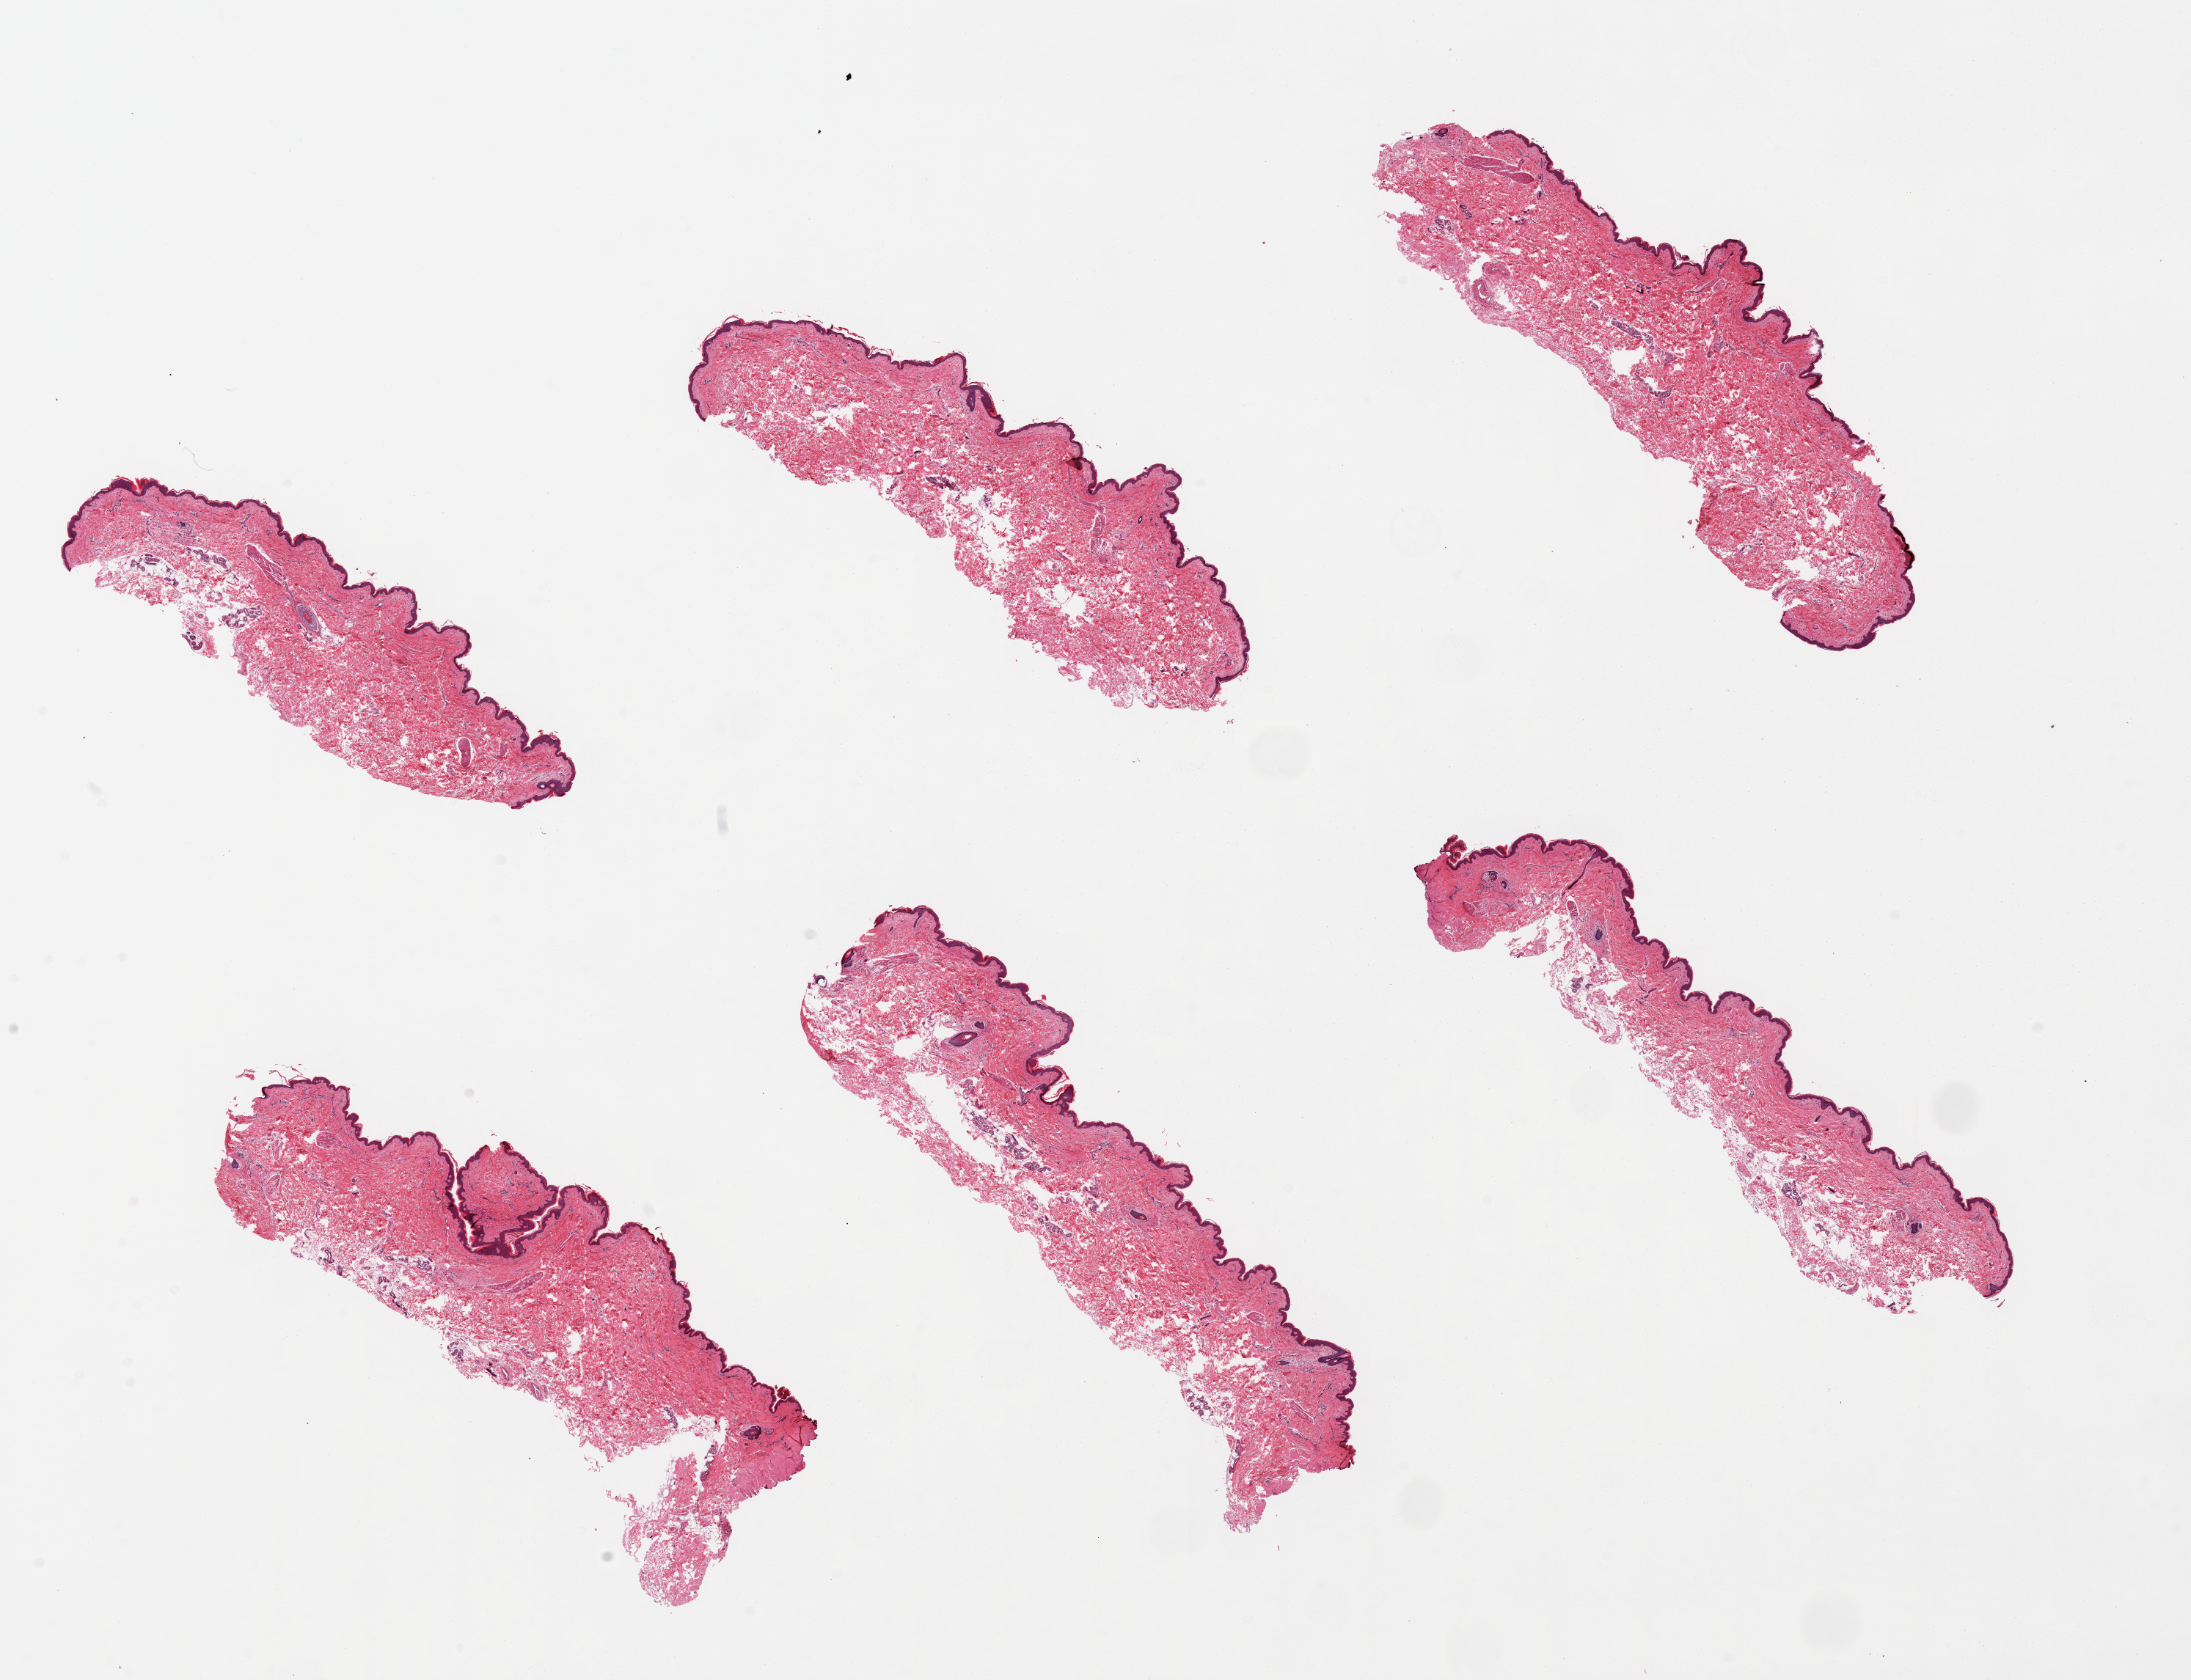
Whole-slide image, hematoxylin and eosin (H&E) stain, shown as a low-resolution overview of the whole scanned area (about 23.6 x 18.1 mm), PAXgene-fixed paraffin-embedded (PFPE) section, target tissue: skin of suprapubic region, tissue donor sample. Female donor.
Pathologist's review note for this sample: 6 pieces, up to 8x2.5mm.